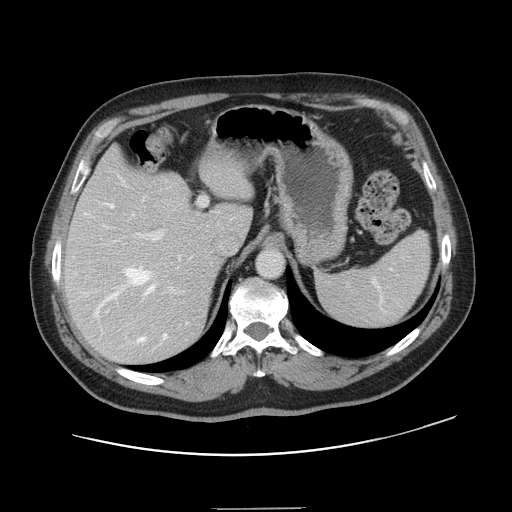
Contrast-enhanced abdominal CT, one axial slice. Position 99 of 143 along the scan axis. 120 kVp. Intravenous contrast given. Soft-tissue window (W 400 / L 40 HU). 512 × 512 image matrix, field of view 402 × 402 mm. Male patient, age 62 years. From the clinical record (not read from this slice): diagnosis: colorectal cancer liver metastases, imaged before liver resection; multiple liver metastases: yes; largest metastasis: 2.7 cm; disease in both lobes: no.
Outlined on this slice (outlined manually by an expert reader):
- hepatic veins: bounding box (x1, y1, x2, y2) in pixels: (85, 180, 180, 342)
- liver: (66, 150, 251, 363)
- planned liver remnant (the part of the liver to remain after resection): (66, 150, 251, 261)
- portal vein (with intrahepatic branches): (107, 198, 207, 293)